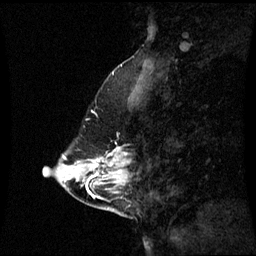
Breast MRI (dynamic contrast-enhanced), one sagittal slice. Dynamic contrast-enhanced series, image 2 of 3 at this slice position (ordered by acquisition). 1.5 T. TE 4.2 ms, TR 8.9 ms. 2.3 mm slice thickness. 256 × 256 image matrix. Female patient, age 43 years. From the clinical record (not read from this slice): setting: breast cancer imaged before/during neoadjuvant chemotherapy; receptor status: HR-positive, HER2-negative.
Structures marked on this image (semi-automatic segmentation, software-assisted and operator-edited):
- analysis volume of interest (the breast-tissue region the enhancement analysis was run in; not a lesion): bounding box [x1, y1, x2, y2] px = [78, 148, 129, 193]
- tumour enhancement mask (voxels above the 70 % enhancement threshold inside the analysis volume of interest): [96, 160, 104, 177]